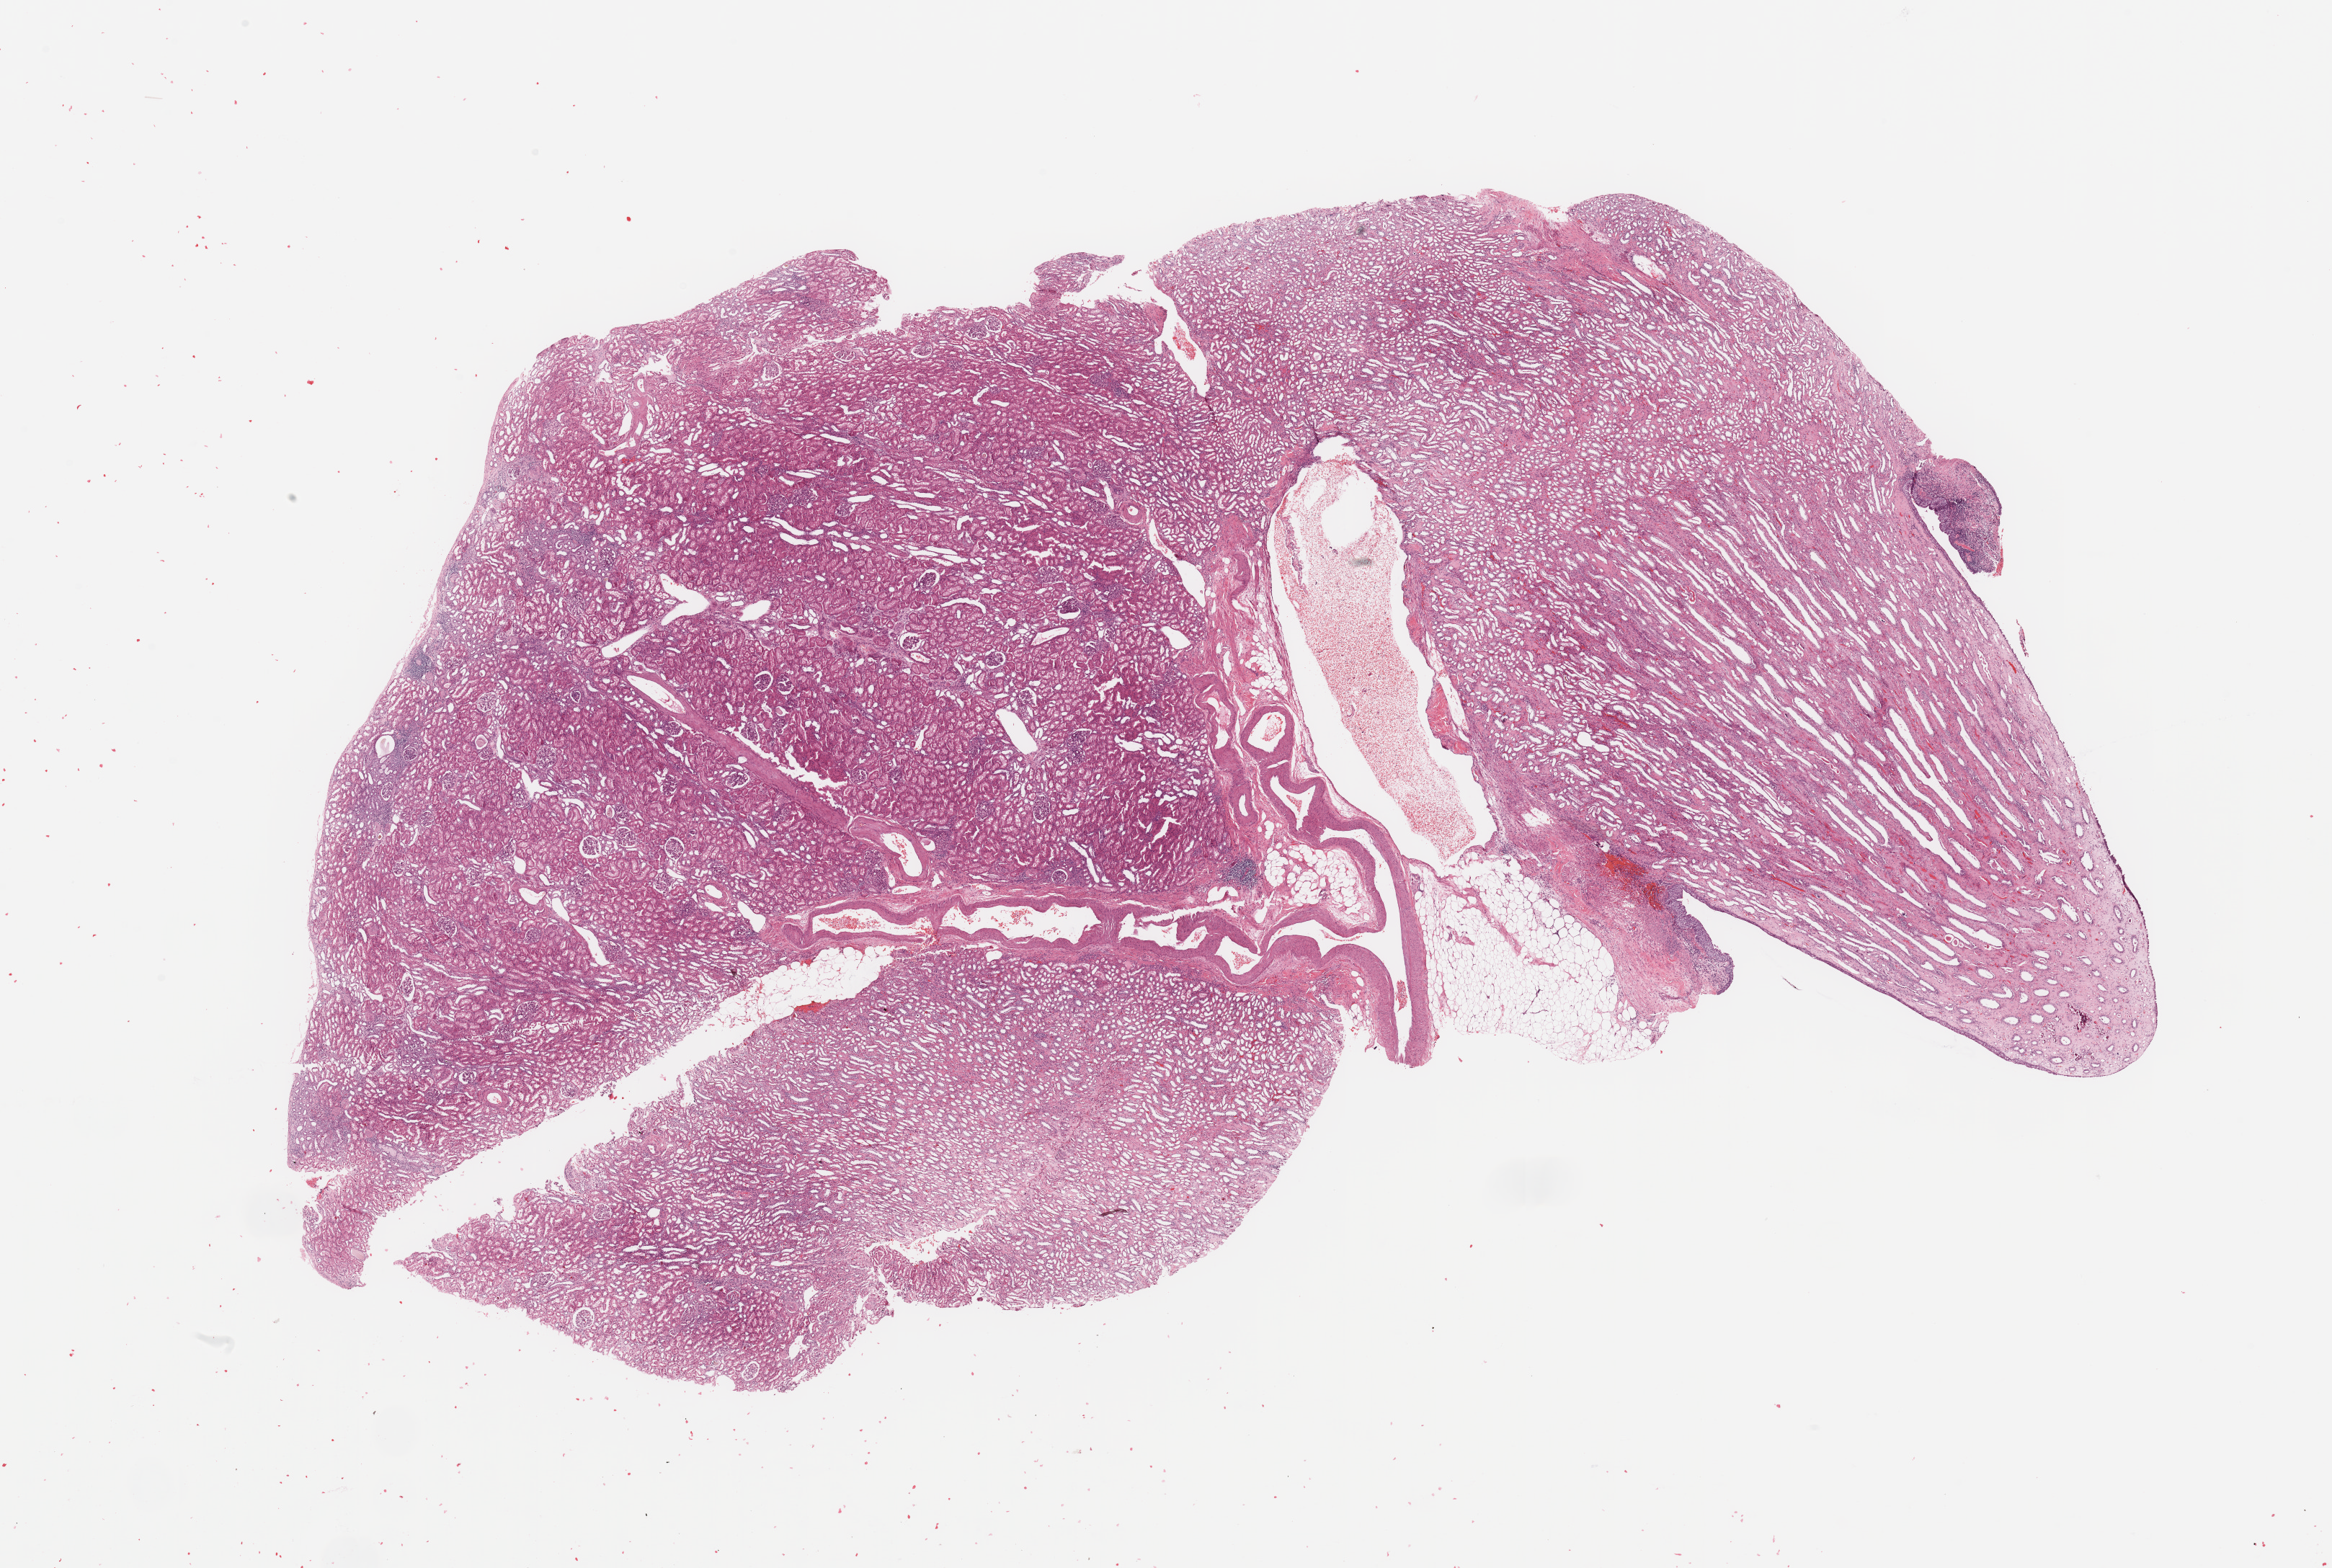
Digitized H&E tissue section (whole slide) — shown as a low-resolution overview of the whole scanned area (about 25.6 x 17.2 mm, slide scanned at 20x); kidney, normal (non-tumour) tissue. 69-year-old female patient.
• this section: normal (non-tumour) tissue from the same patient
• patient diagnosis: Renal cell carcinoma, NOS